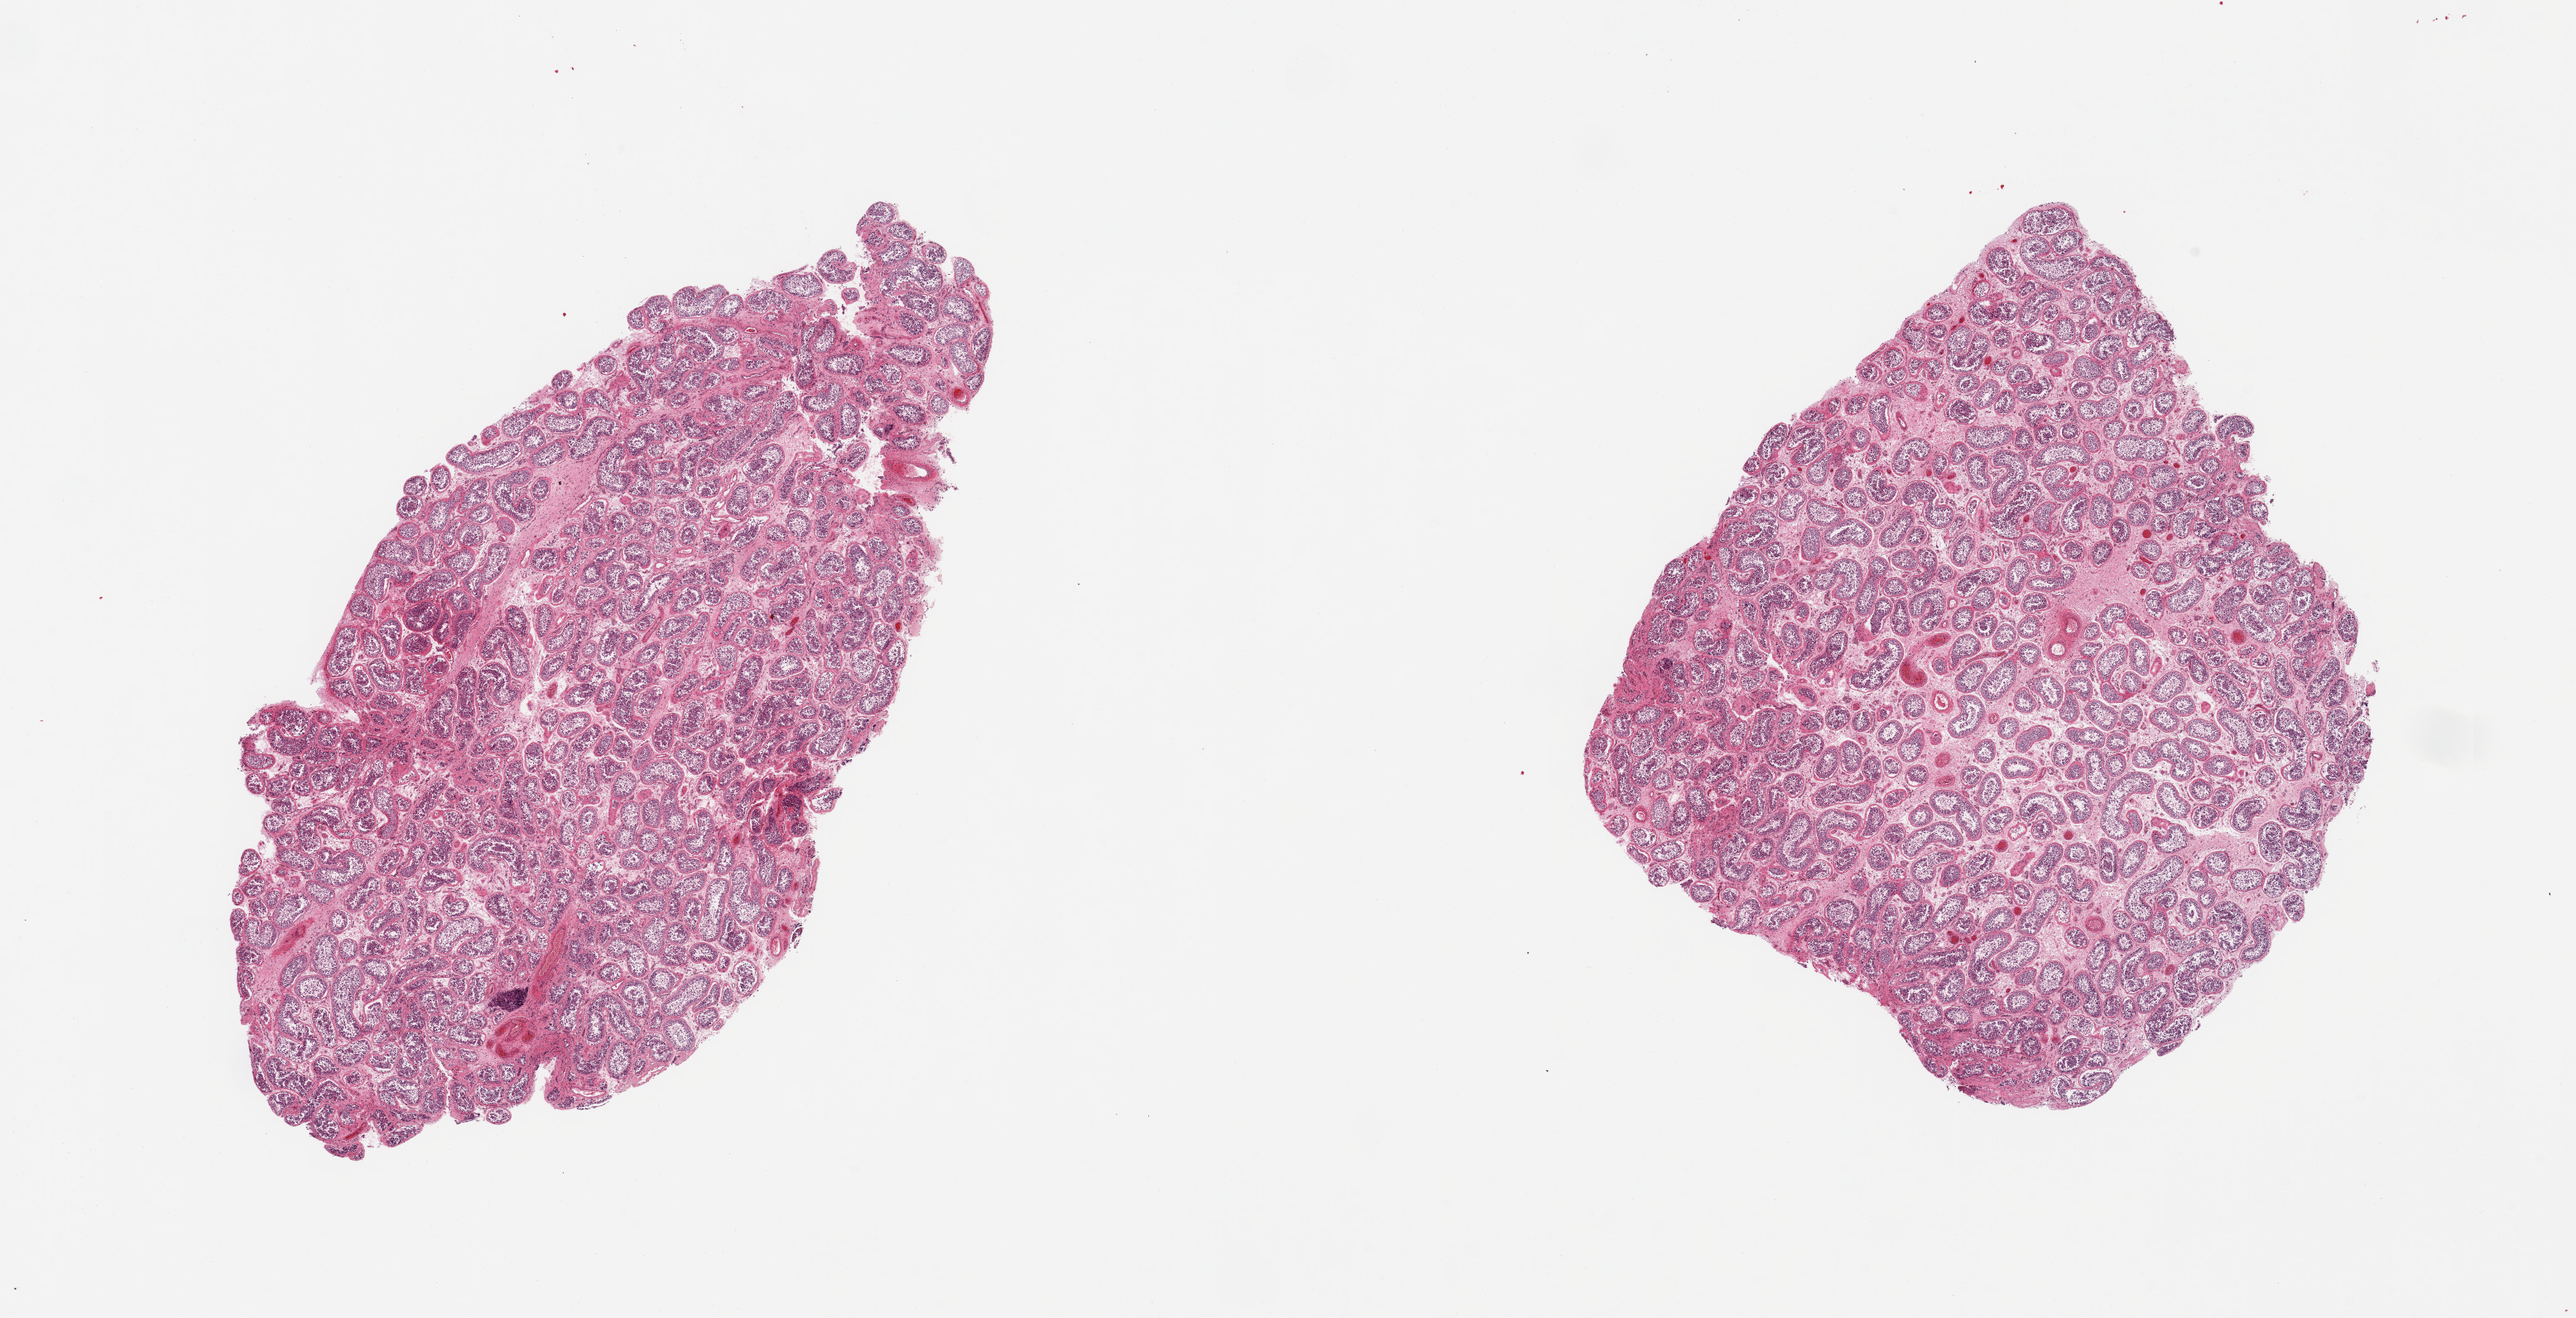
Whole-slide image, H&E stain, whole scanned area (about 24.6 x 12.6 mm) shown as a low-resolution overview. PAXgene-fixed, paraffin-embedded tissue. Section of testis (target tissue). Tissue donor sample. Male donor.
• pathologist's review note for this sample: 2 pieces; spermatogenesis